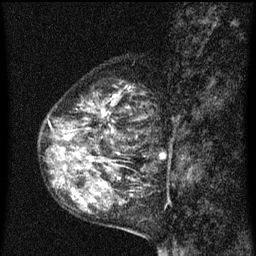
Breast MRI (dynamic contrast-enhanced), one sagittal slice. Slice 26 of 60 in the series (ordered by position). Dynamic contrast-enhanced series, image 2 of 3 at this slice position (ordered by acquisition). 1.5 T. TE 4.2 ms, TR 8 ms. 2 mm slice thickness. 256 × 256 image matrix, field of view 180 × 180 mm. Patient: female, 55 years.
Structures marked on this image (semi-automatic segmentation, software-assisted and operator-edited):
- analysis volume of interest (the breast-tissue region the enhancement analysis was run in; not a lesion): box from (x=40, y=84) to (x=157, y=151) px
- tumour enhancement mask (voxels above the 70 % enhancement threshold inside the analysis volume of interest): (x=60, y=94)–(x=121, y=151)